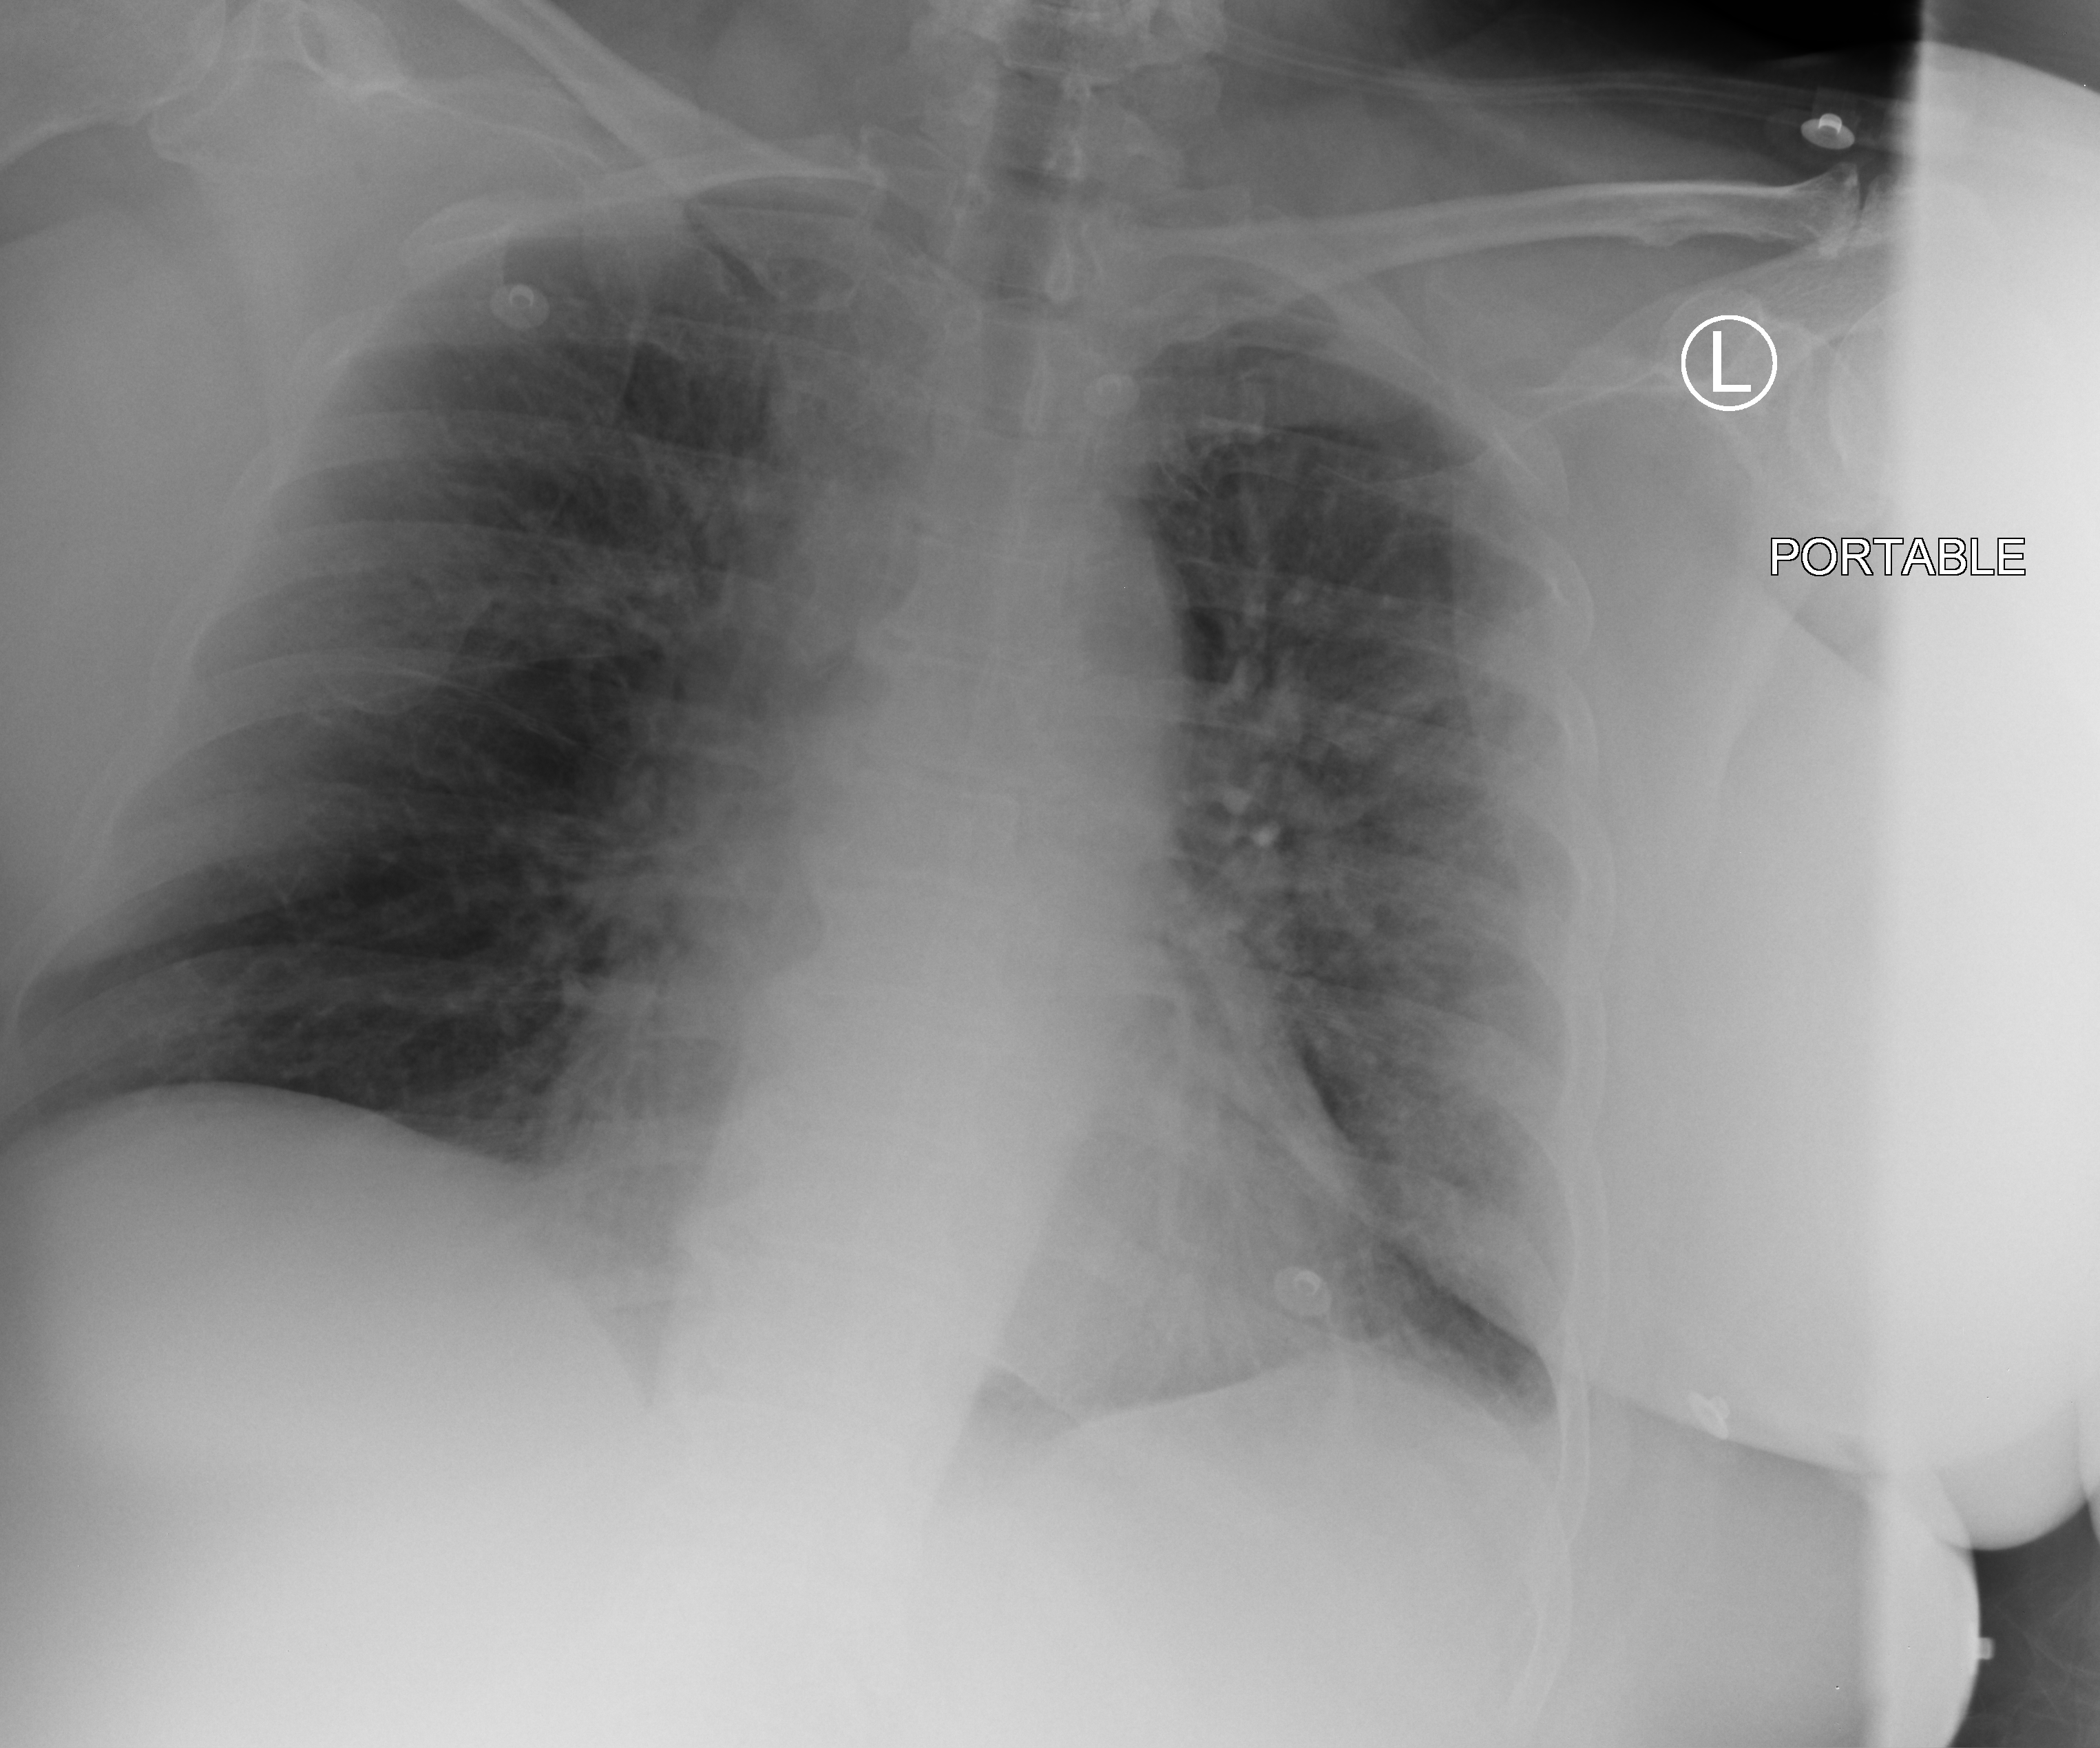
Portable chest radiograph, anteroposterior (AP) projection. Female patient hospitalised with COVID-19, age 60–74 years.
Hospital-stay facts (about this admission, not read from this image; timing relative to this image not recorded):
- hypertension (admission record): yes